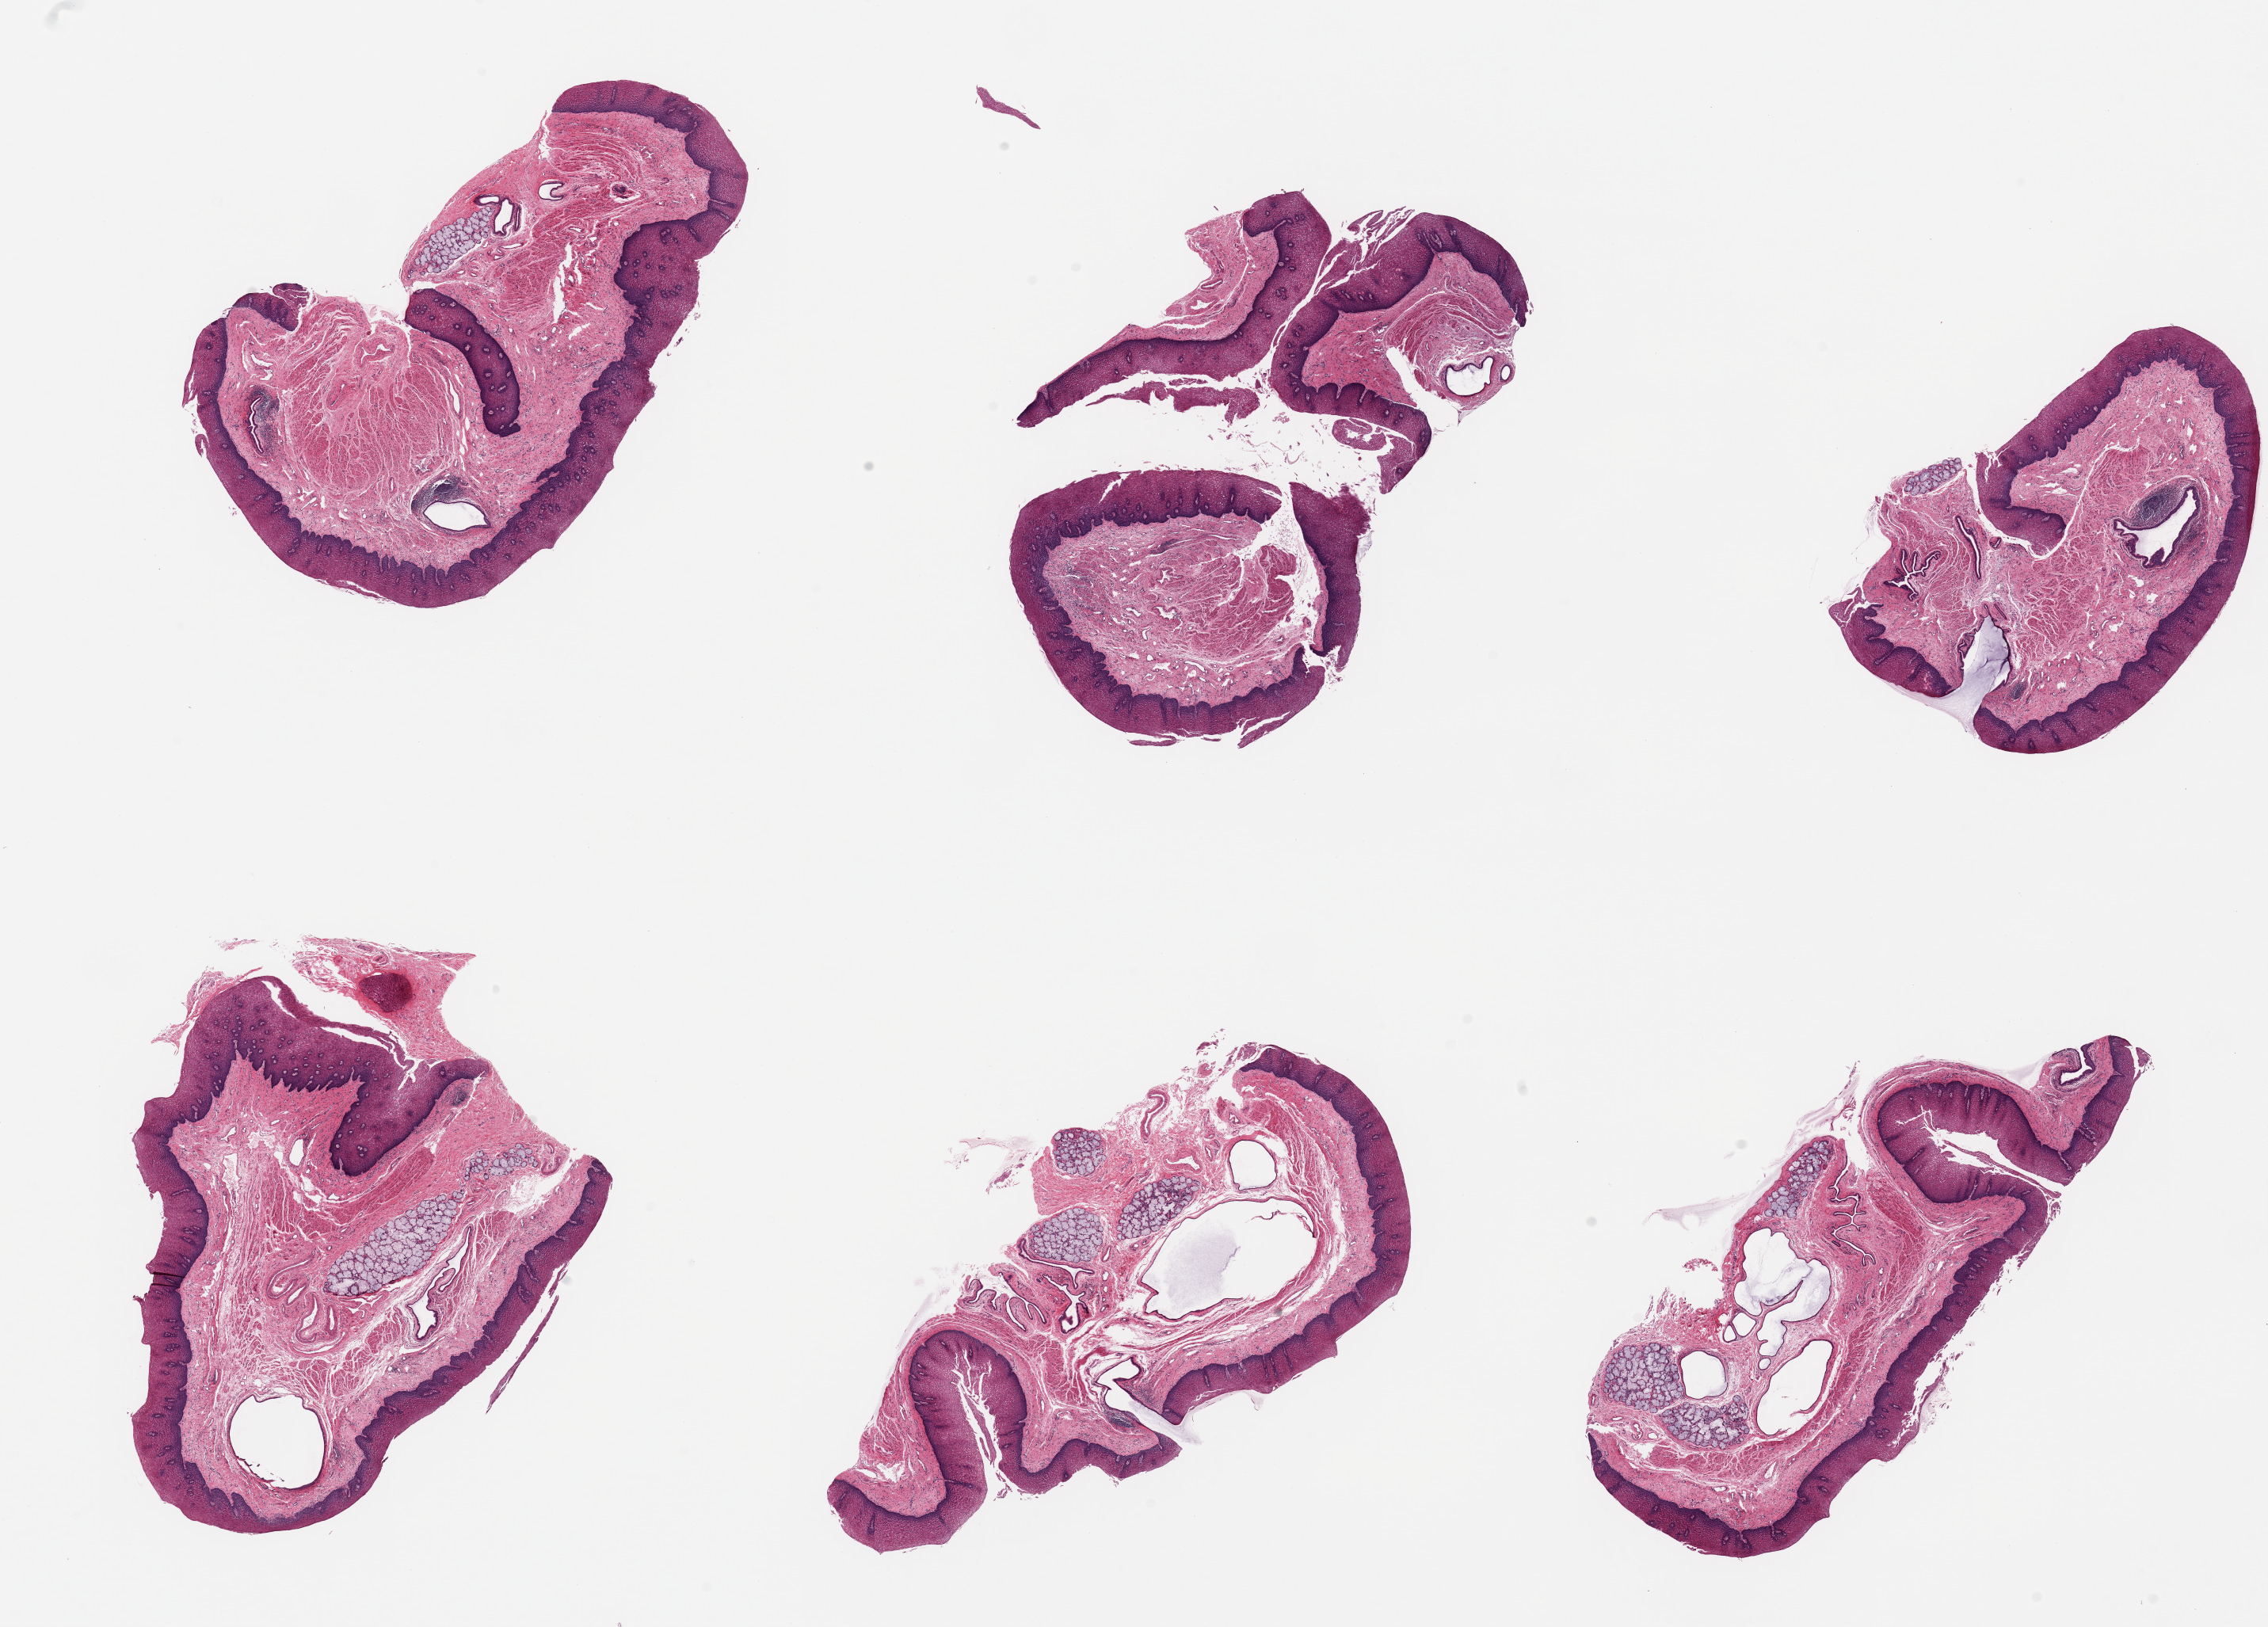
Whole-slide image, H&E stain, shown as a low-resolution overview of the whole scanned area (about 22.6 x 16.2 mm); PAXgene-fixed paraffin-embedded (PFPE) section; section of esophageal mucous membrane (target tissue); tissue donor sample. Donor sex: male.
* pathologist's review note for this sample: 6 pieces, Squamous mucosa up to ~0.4mm, ~15% thickness; numerous submucosal mucus glands